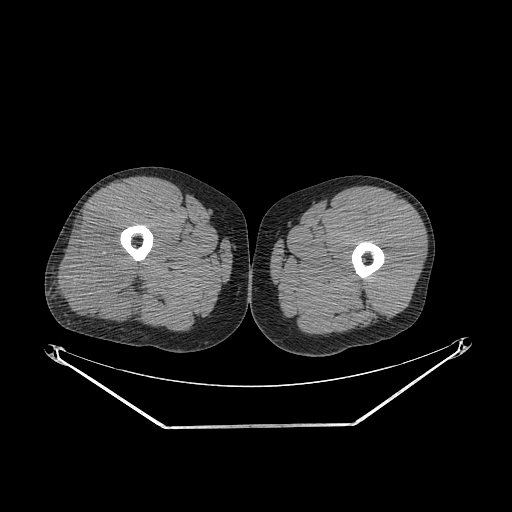
CT of an extremity soft-tissue mass (from a PET/CT study), one axial slice; slice 251 of 267 in the series (ordered by position); reconstruction kernel STANDARD; soft-tissue window (W 400 / L 40 HU); 512 × 512 image matrix, field of view 500 × 500 mm. Male patient. Case-level facts recorded for this patient, not image findings: histological type: poorly differentiated synovial sarcoma; grade: high; site of the primary tumour: right buttock.
Outlined on this slice (expert contour drawn on MRI and transferred to this co-registered scan by the dataset authors):
- gross tumour volume including surrounding oedema: bounding box <60,219,147,318> (left, top, right, bottom; pixels)
- gross tumour volume (mass): <60,219,143,318>